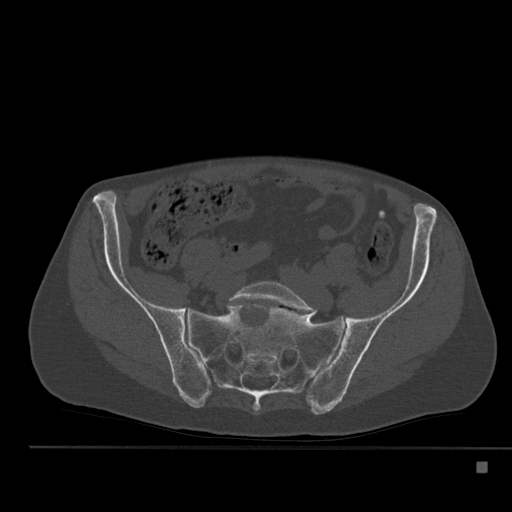
CT including the spine, one axial slice. Slice 103 of 517 in the series (ordered by position). 120 kVp. Bone window (W 1800 / L 400 HU). 1.5 mm slice thickness. 512 × 512 image matrix, field of view 408 × 408 mm. Male patient, age 70 years. Case-level facts recorded for this patient, not image findings: primary cancer: renal; vertebrae with lytic lesions (as recorded): T4, T6, T10, T12, L3, L4, L5.
Structures marked on this image (semi-automatic segmentation, software-assisted and operator-edited):
- L5 vertebra: box from (x=229, y=281) to (x=316, y=315) px